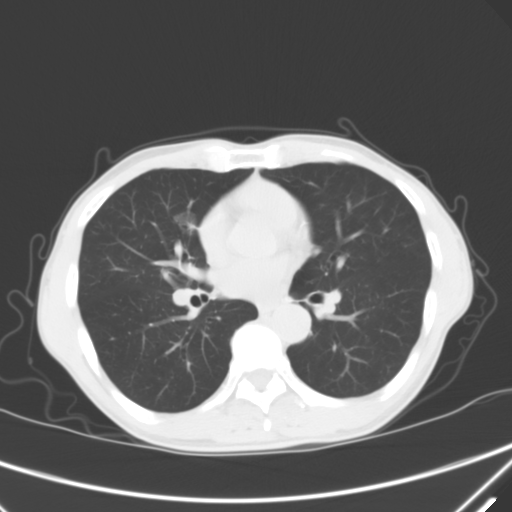
Chest CT, one axial slice; position 34 of 68 along the scan axis; 120 kVp; lung window (W 1500 / L -600 HU); 5 mm slice thickness; 512 × 512 image matrix. Male patient, age 67 years. Case-level facts recorded for this patient, not image findings: clinical TNM (as recorded): T1c N0 M0.
Outlined on this slice (rectangle marked by the reading radiologist):
- lung tumour (recorded histology: adenocarcinoma): box from (x=172, y=203) to (x=201, y=245) px